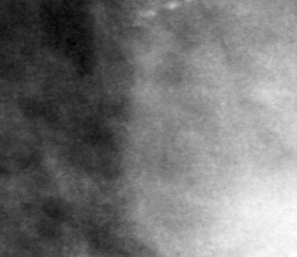
Cropped region of a digitized screen-film mammogram centred on a radiologist-marked abnormality; right breast; MLO view; BI-RADS breast density category 3 (scale 1–4).
- Calcifications, morphology pleomorphic, distribution clustered; BI-RADS assessment category 4; subtlety rating 2 on a 1 (subtle) to 5 (obvious) scale; pathology result (as recorded, not read from the image): benign.